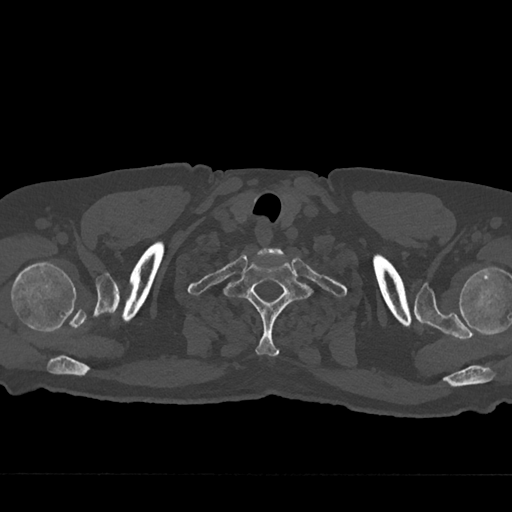
CT including the spine, one axial slice; slice 659 of 797 in the series (ordered by position); reconstruction kernel Br40s/3; 120 kVp; bone window (W 1800 / L 400 HU); 0.5 mm slice thickness; 512 × 512 image matrix. Patient: male, 75 years. Case-level facts recorded for this patient, not image findings: primary cancer: renal.
Structures marked on this image (semi-automatically segmented with operator editing):
- T1 vertebra: bounding box (x1, y1, x2, y2) in pixels: (223, 261, 314, 356)
- T2 vertebra: (279, 292, 284, 298)